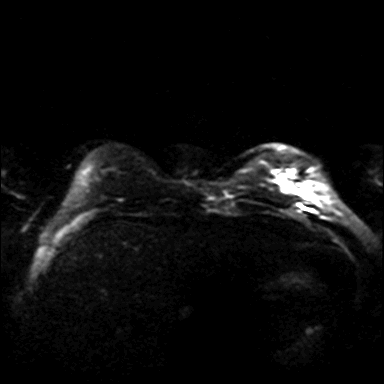
Breast MRI, one axial slice. Slice 6 of 36 in the series (ordered by position). Diffusion-weighted series; image 2 of 4 stored at this slice position (different b-values; order by instance number). 3 T. 4 mm slice thickness. 384 × 384 image matrix, field of view 320 × 320 mm. Female patient.
Outlined on this slice (manually delineated by an expert):
- tumour on diffusion-weighted imaging: bounding box [x1, y1, x2, y2] px = [278, 170, 294, 191]